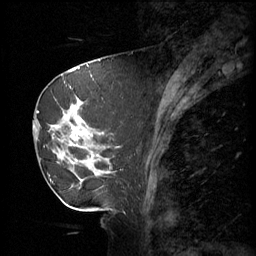
Breast MRI (dynamic contrast-enhanced), one sagittal slice; slice 21 of 60 in the series (ordered by position); 3 images stored at this slice position (order not interpretable as contrast timing); 1.5 T; TE 4.2 ms, TR 11 ms; 2 mm slice thickness; 256 × 256 image matrix. Patient: female, 69 years.
Structures marked on this image (semi-automatically segmented with operator editing):
- analysis volume of interest (the breast-tissue region the enhancement analysis was run in; not a lesion): bounding box <36,88,116,189> (left, top, right, bottom; pixels)
- tumour enhancement mask (voxels above the 70 % enhancement threshold inside the analysis volume of interest): <52,98,103,183>